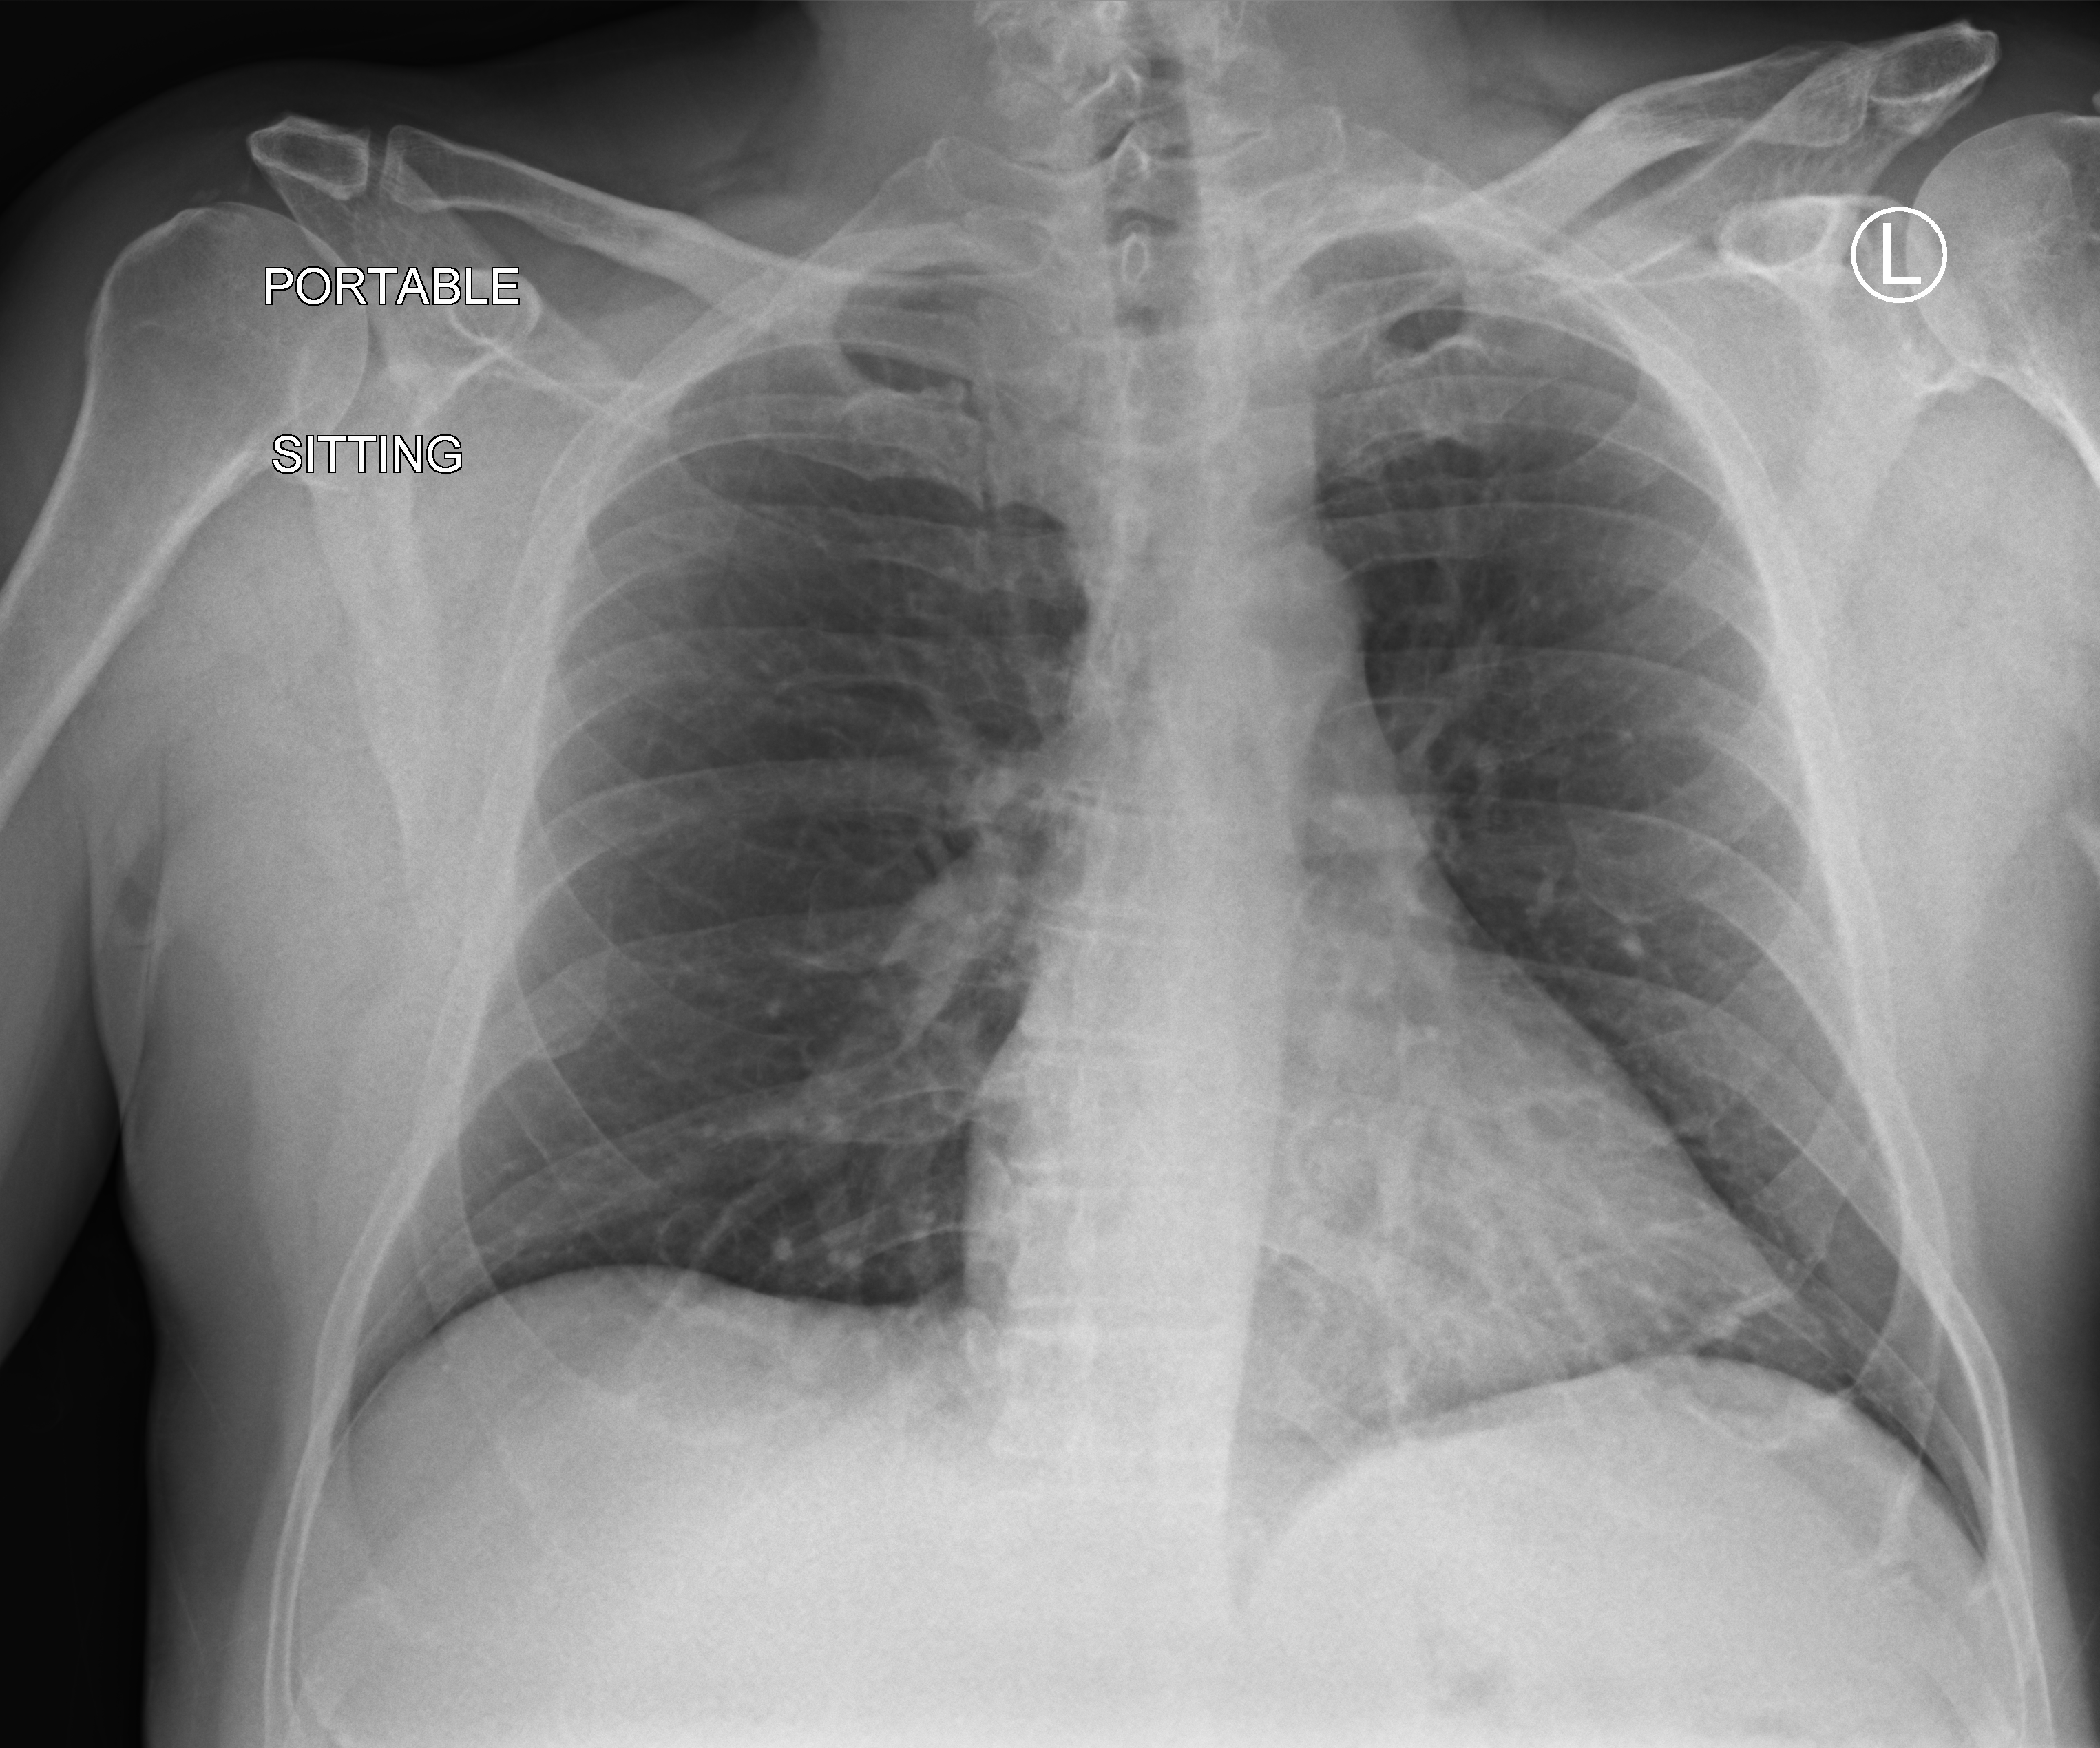
Bedside chest radiograph (computed radiography), anteroposterior (AP) projection. Patient hospitalised with COVID-19; male, aged 18–59 years.
Hospital-stay facts (about this admission, not read from this image; timing relative to this image not recorded): admitted to intensive care during this hospital stay: yes.